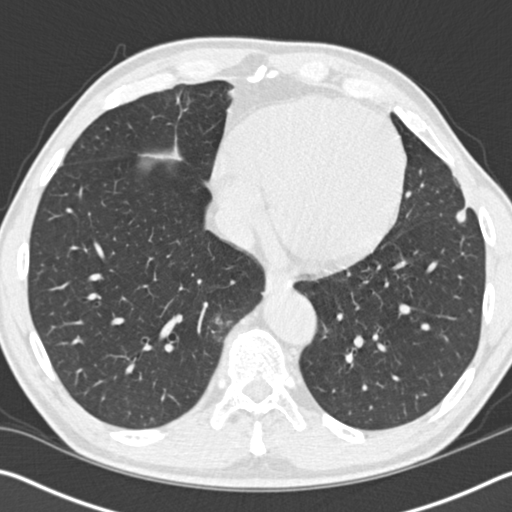
Low-dose screening chest CT, one axial slice. Slice 47 of 162 in the series (ordered by position). Reconstruction kernel B30f. 120 kVp. Lung window (W 1500 / L -600 HU). 2 mm slice thickness. 512 × 512 image matrix, field of view 340 × 340 mm.
Structures marked on this image (expert manual segmentation):
- lesion 1 (tumor, upper lobe of left lung): bounding box <456,206,468,223> (left, top, right, bottom; pixels)